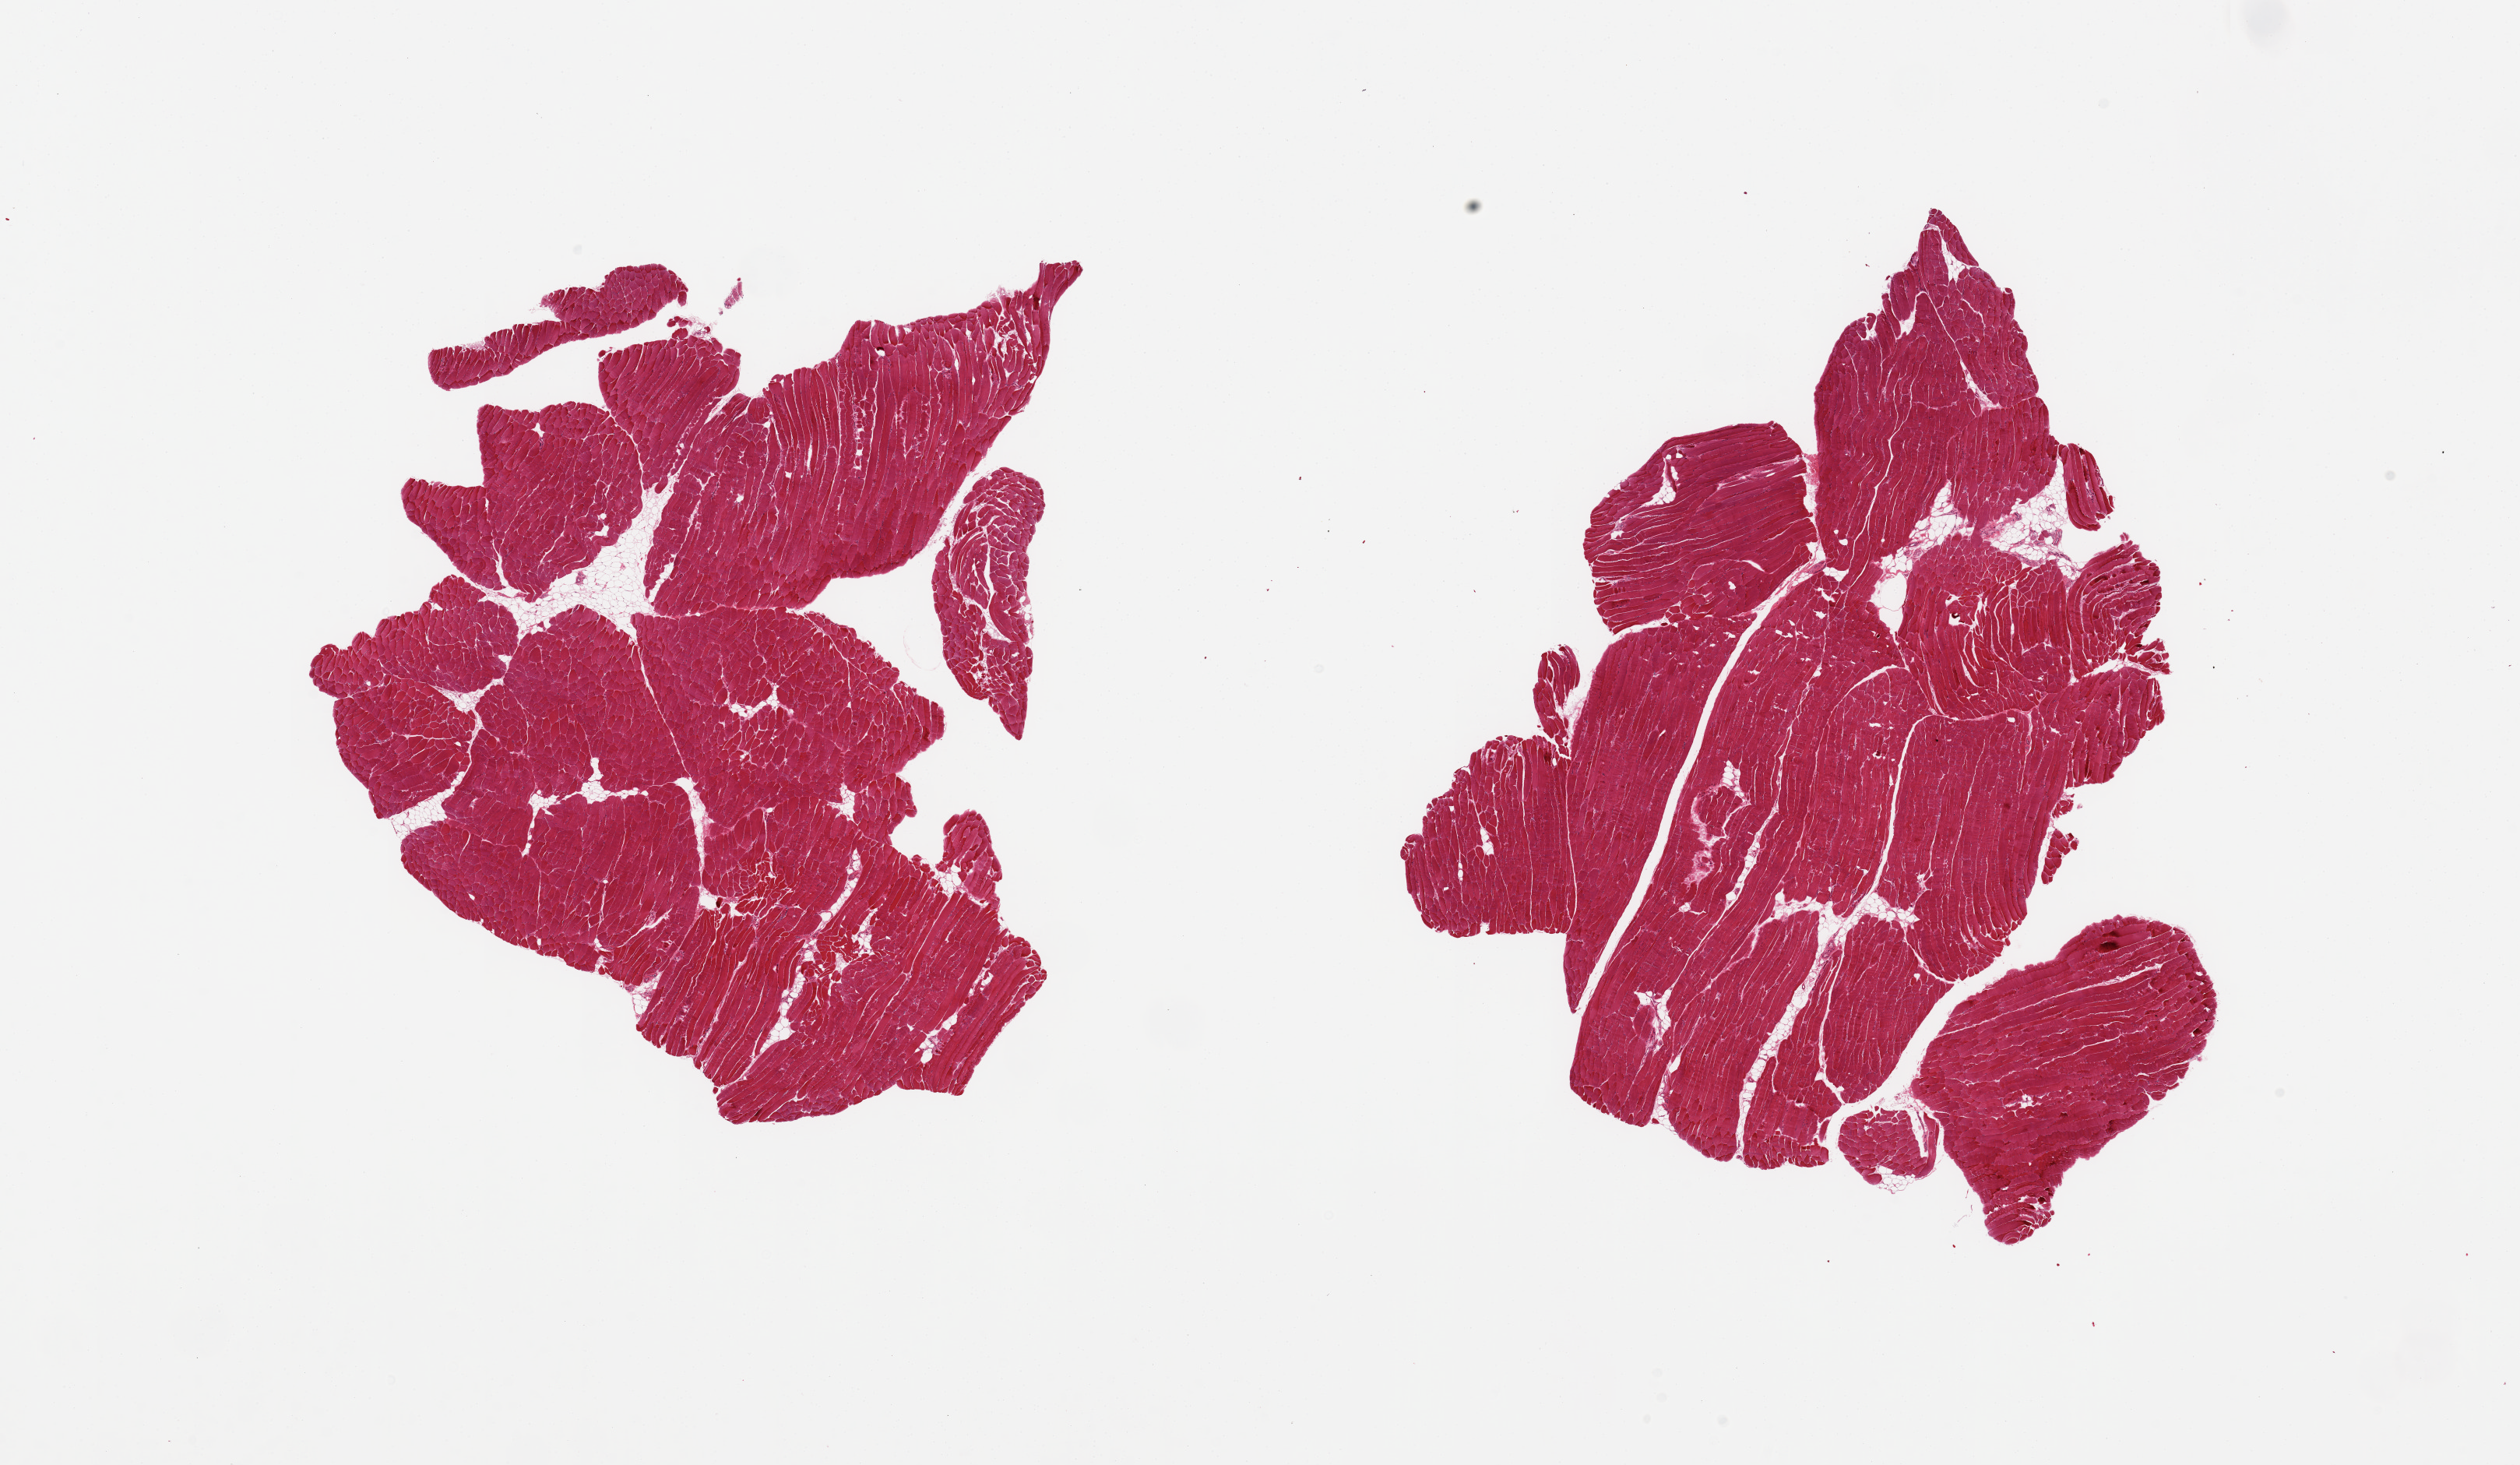
H&E whole-slide image, shown as a low-resolution overview of the whole scanned area (about 25.6 x 14.9 mm). PAXgene-fixed paraffin-embedded (PFPE) section. Section of skeletal muscle (target tissue). Tissue donor sample. Female donor.
Review note (as recorded): 2 pieces; <10% internal fat.